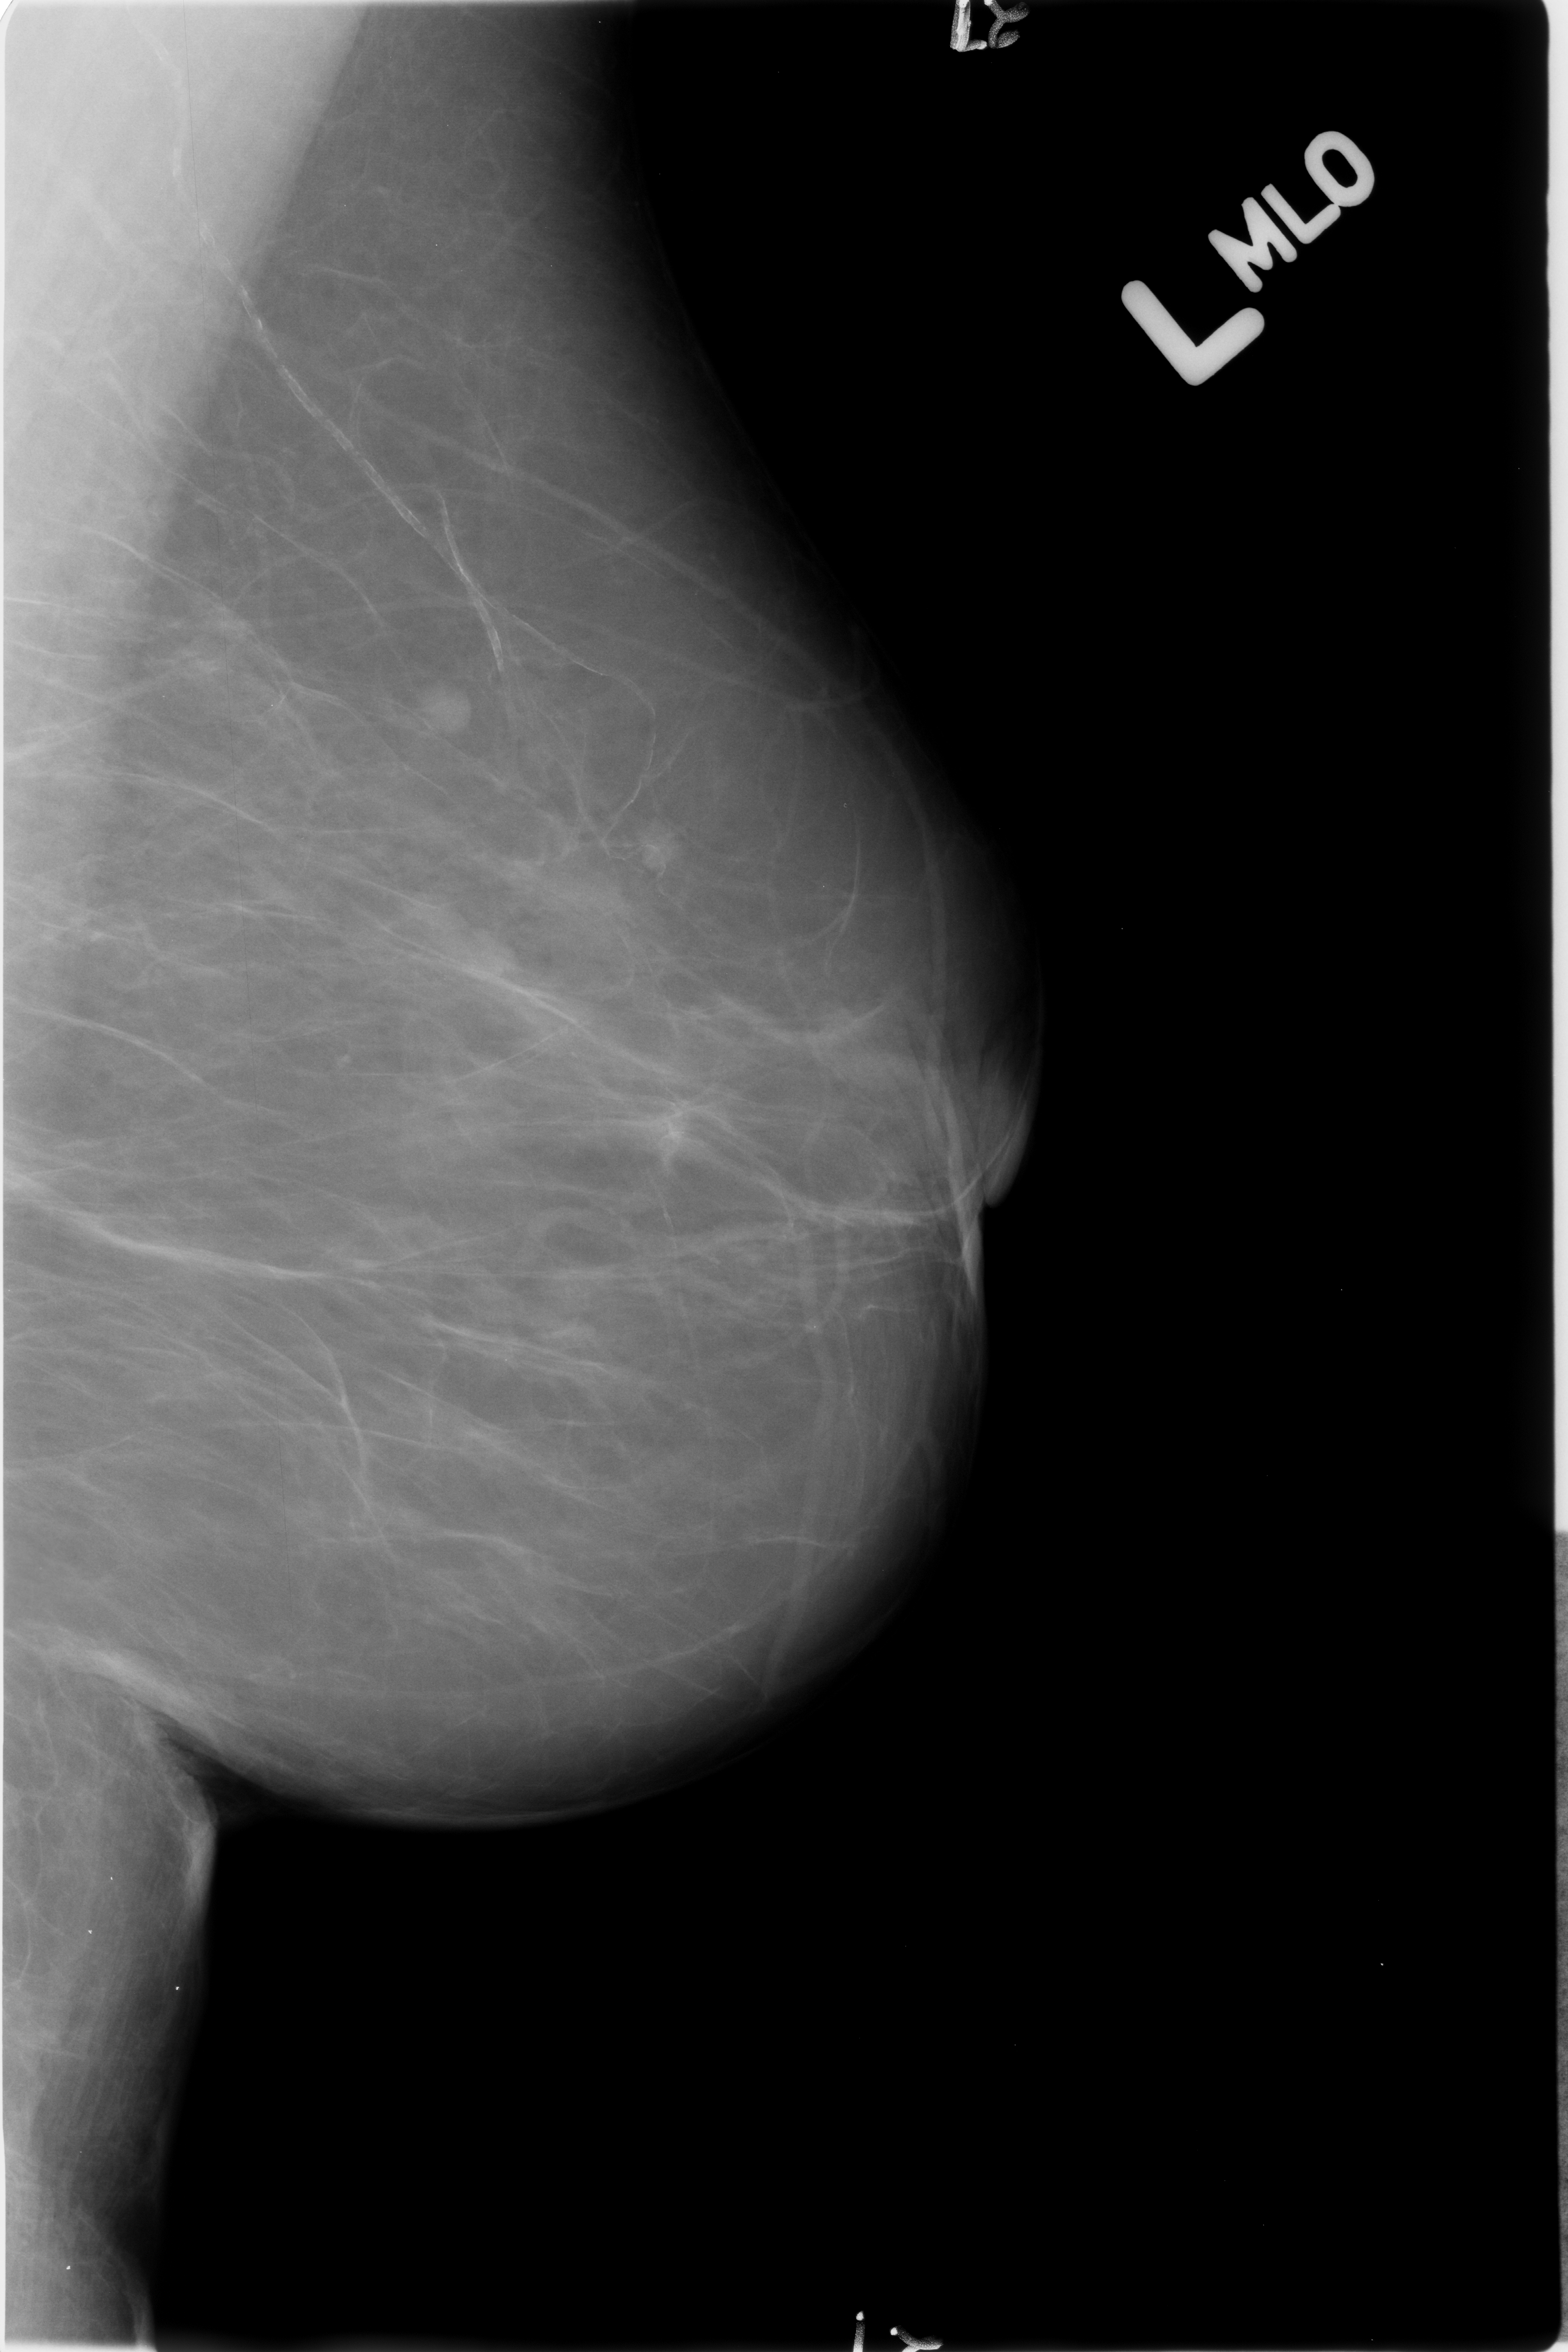
Mammogram (digitized film), left breast, MLO view.
Marked findings (only marked abnormalities are described; nothing is implied about the rest of the image): calcifications, morphology vascular; BI-RADS assessment category 2; subtlety rating 4 on a 1 (subtle) to 5 (obvious) scale; benign; no additional work-up was recommended (benign without callback).